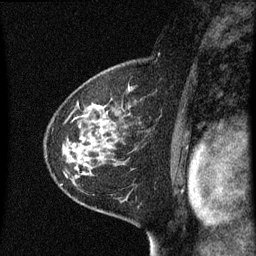
Breast MRI (dynamic contrast-enhanced), one sagittal slice; slice 40 of 60 in the series (ordered by position); dynamic contrast-enhanced series, image 2 of 3 at this slice position (ordered by acquisition); 1.5 T; TE 4.2 ms, TR 8 ms; 256 × 256 image matrix. Patient: female, 60 years.
Annotated regions visible in this slice (semi-automatically segmented with operator editing):
- analysis volume of interest (the breast-tissue region the enhancement analysis was run in; not a lesion): bounding box <48,82,143,183> (left, top, right, bottom; pixels)
- tumour enhancement mask (voxels above the 70 % enhancement threshold inside the analysis volume of interest): <98,108,109,133>